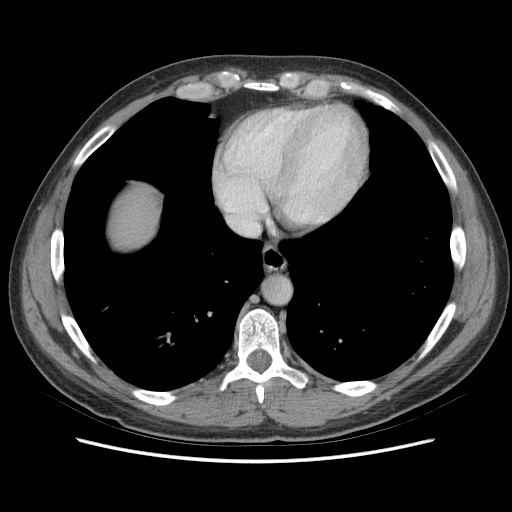
Contrast-enhanced abdominal CT (liver protocol), one axial slice. Slice 70 of 73 in the series (ordered by position). 140 kVp. Soft-tissue window (W 400 / L 40 HU). 512 × 512 image matrix. Case-level facts recorded for this patient, not image findings: diagnosis: hepatocellular carcinoma (patient treated with transarterial chemoembolisation; whether this scan precedes or follows treatment is not stated here); TNM stage (as recorded): Stage-IIIA; Child-Pugh class: A; tumour nodularity: multinodular; tumour size: 6.6 cm.
Outlined on this slice (semi-automatic segmentation, software-assisted and operator-edited):
- abdominal aorta: bounding box <264,277,290,304> (left, top, right, bottom; pixels)
- liver parenchyma outside the tumour (the mass and vessels are separate outlines, so this box may not span the whole liver): <112,188,158,246>